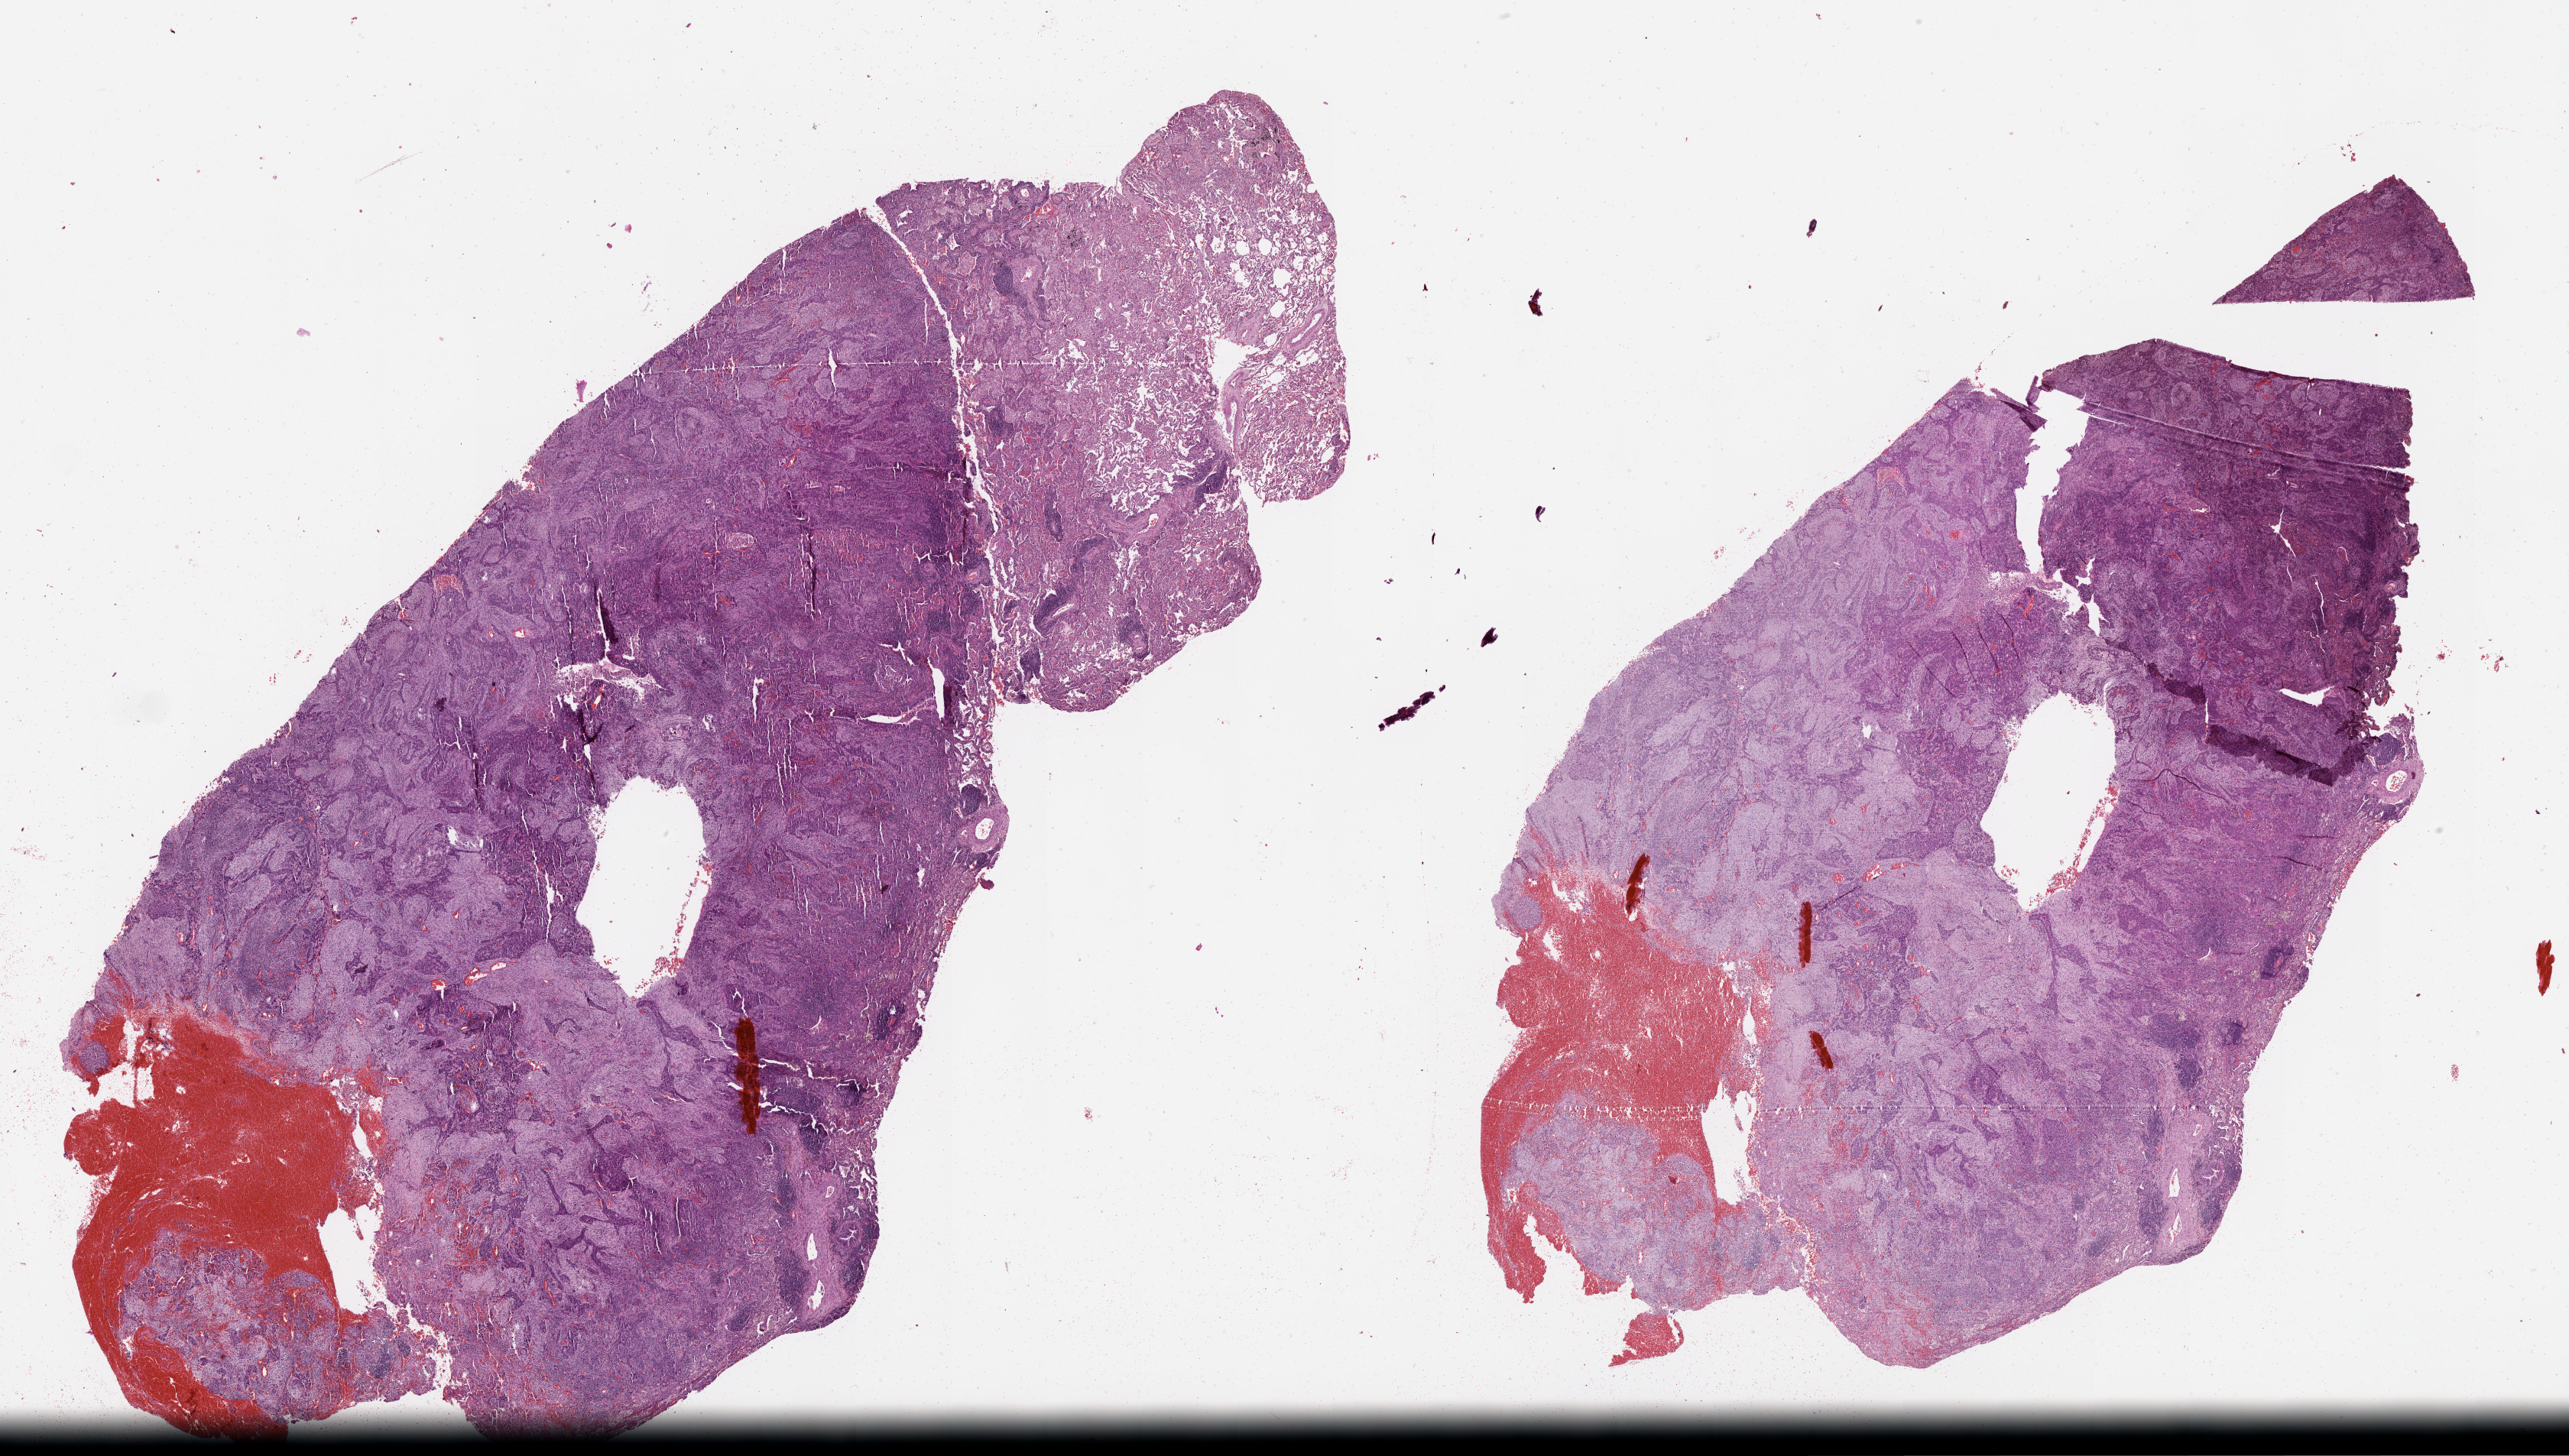
Whole-slide histology image, H&E-stained — a low-resolution overview of the entire scanned area, about 27.1 x 15.3 mm, tumour tissue sample, lung. Patient: female, age 62 years.
Patient diagnosis (cohort enrolment): squamous cell carcinoma (lung).